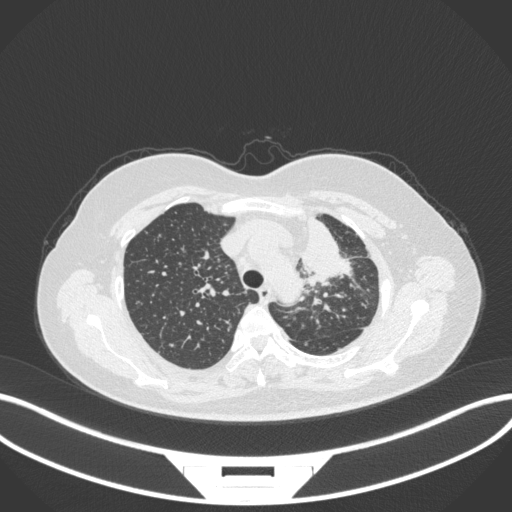
Chest CT, one axial slice. Position 257 of 348 along the scan axis. Reconstruction kernel B31f. Lung window (W 1500 / L -600 HU). 512 × 512 image matrix, field of view 400 × 400 mm. Female patient, age 49 years. From the clinical record (not read from this slice): clinical TNM (as recorded): T1c N0 M1.
Structures marked on this image (rectangle marked by the reading radiologist):
- lung tumour (recorded histology: adenocarcinoma): bounding box (x1, y1, x2, y2) in pixels: (293, 203, 356, 294)